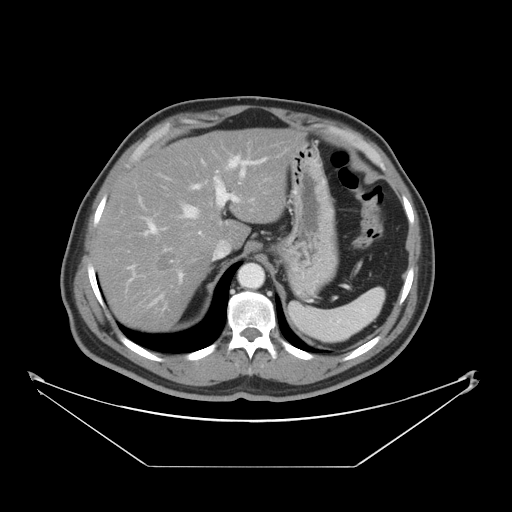
Contrast-enhanced abdominal CT, one axial slice; position 33 of 46 along the scan axis; intravenous contrast given; soft-tissue window (W 400 / L 40 HU); 5 mm slice thickness; 512 × 512 image matrix, field of view 465 × 465 mm. Male patient, age 57 years. From the clinical record (not read from this slice): diagnosis: colorectal cancer liver metastases, imaged before liver resection; multiple liver metastases: no; largest metastasis: 3.3 cm; chemotherapy before resection: yes.
Structures marked on this image (expert manual segmentation):
- hepatic veins: bounding box [x1, y1, x2, y2] px = [182, 205, 200, 219]
- liver: [96, 130, 300, 330]
- planned liver remnant (the part of the liver to remain after resection): [96, 129, 300, 324]
- portal vein (with intrahepatic branches): [130, 156, 265, 301]
- liver metastasis: [155, 250, 178, 274]